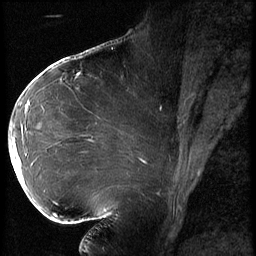
Breast MRI (dynamic contrast-enhanced), one sagittal slice. Position 35 of 62 along the scan axis. 3 images stored at this slice position (order not interpretable as contrast timing). 1.5 T. TE 4.2 ms, TR 9 ms. 256 × 256 image matrix, field of view 180 × 180 mm. Patient: female, 43 years. Case-level facts recorded for this patient, not image findings: setting: breast cancer imaged before/during neoadjuvant chemotherapy; receptor status: HER2-positive.
Outlined on this slice (semi-automatically segmented with operator editing):
- analysis volume of interest (the breast-tissue region the enhancement analysis was run in; not a lesion): bounding box <9,90,82,203> (left, top, right, bottom; pixels)
- tumour enhancement mask (voxels above the 140 % enhancement threshold inside the analysis volume of interest): <11,103,29,184>